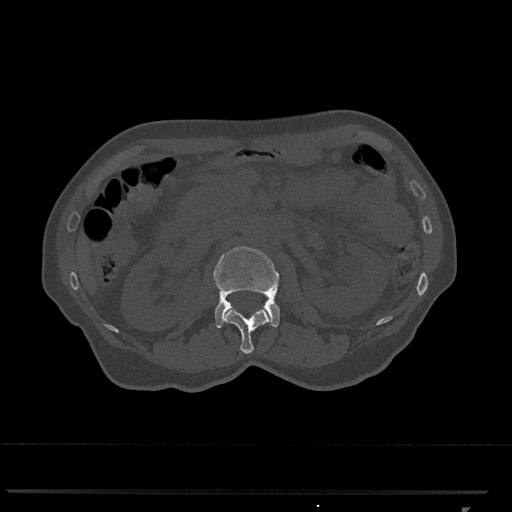
CT including the spine, one axial slice; 120 kVp; bone window (W 1800 / L 400 HU); 512 × 512 image matrix. Female patient, age 62 years. Case-level facts recorded for this patient, not image findings: primary cancer: renal.
Outlined on this slice (semi-automatically segmented with operator editing):
- L1 vertebra: box from (x=222, y=306) to (x=271, y=354) px
- L2 vertebra: (x=214, y=246)–(x=280, y=328)